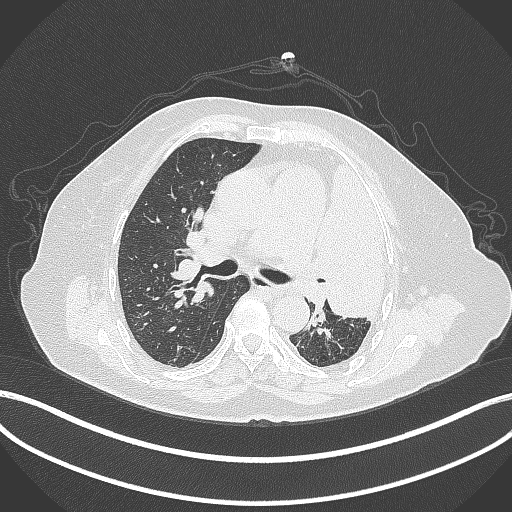
Chest CT, one axial slice. Slice 239 of 399 in the series (ordered by position). Reconstruction kernel B70f. 120 kVp. Lung window (W 1500 / L -600 HU). 1 mm slice thickness. 512 × 512 image matrix, field of view 400 × 400 mm. Patient: female, 75 years. Case-level facts recorded for this patient, not image findings: clinical TNM (as recorded): T3 N3 M1.
Structures marked on this image (bounding box drawn by a radiologist):
- lung tumour (recorded histology: adenocarcinoma): bounding box (x1, y1, x2, y2) in pixels: (315, 162, 387, 320)